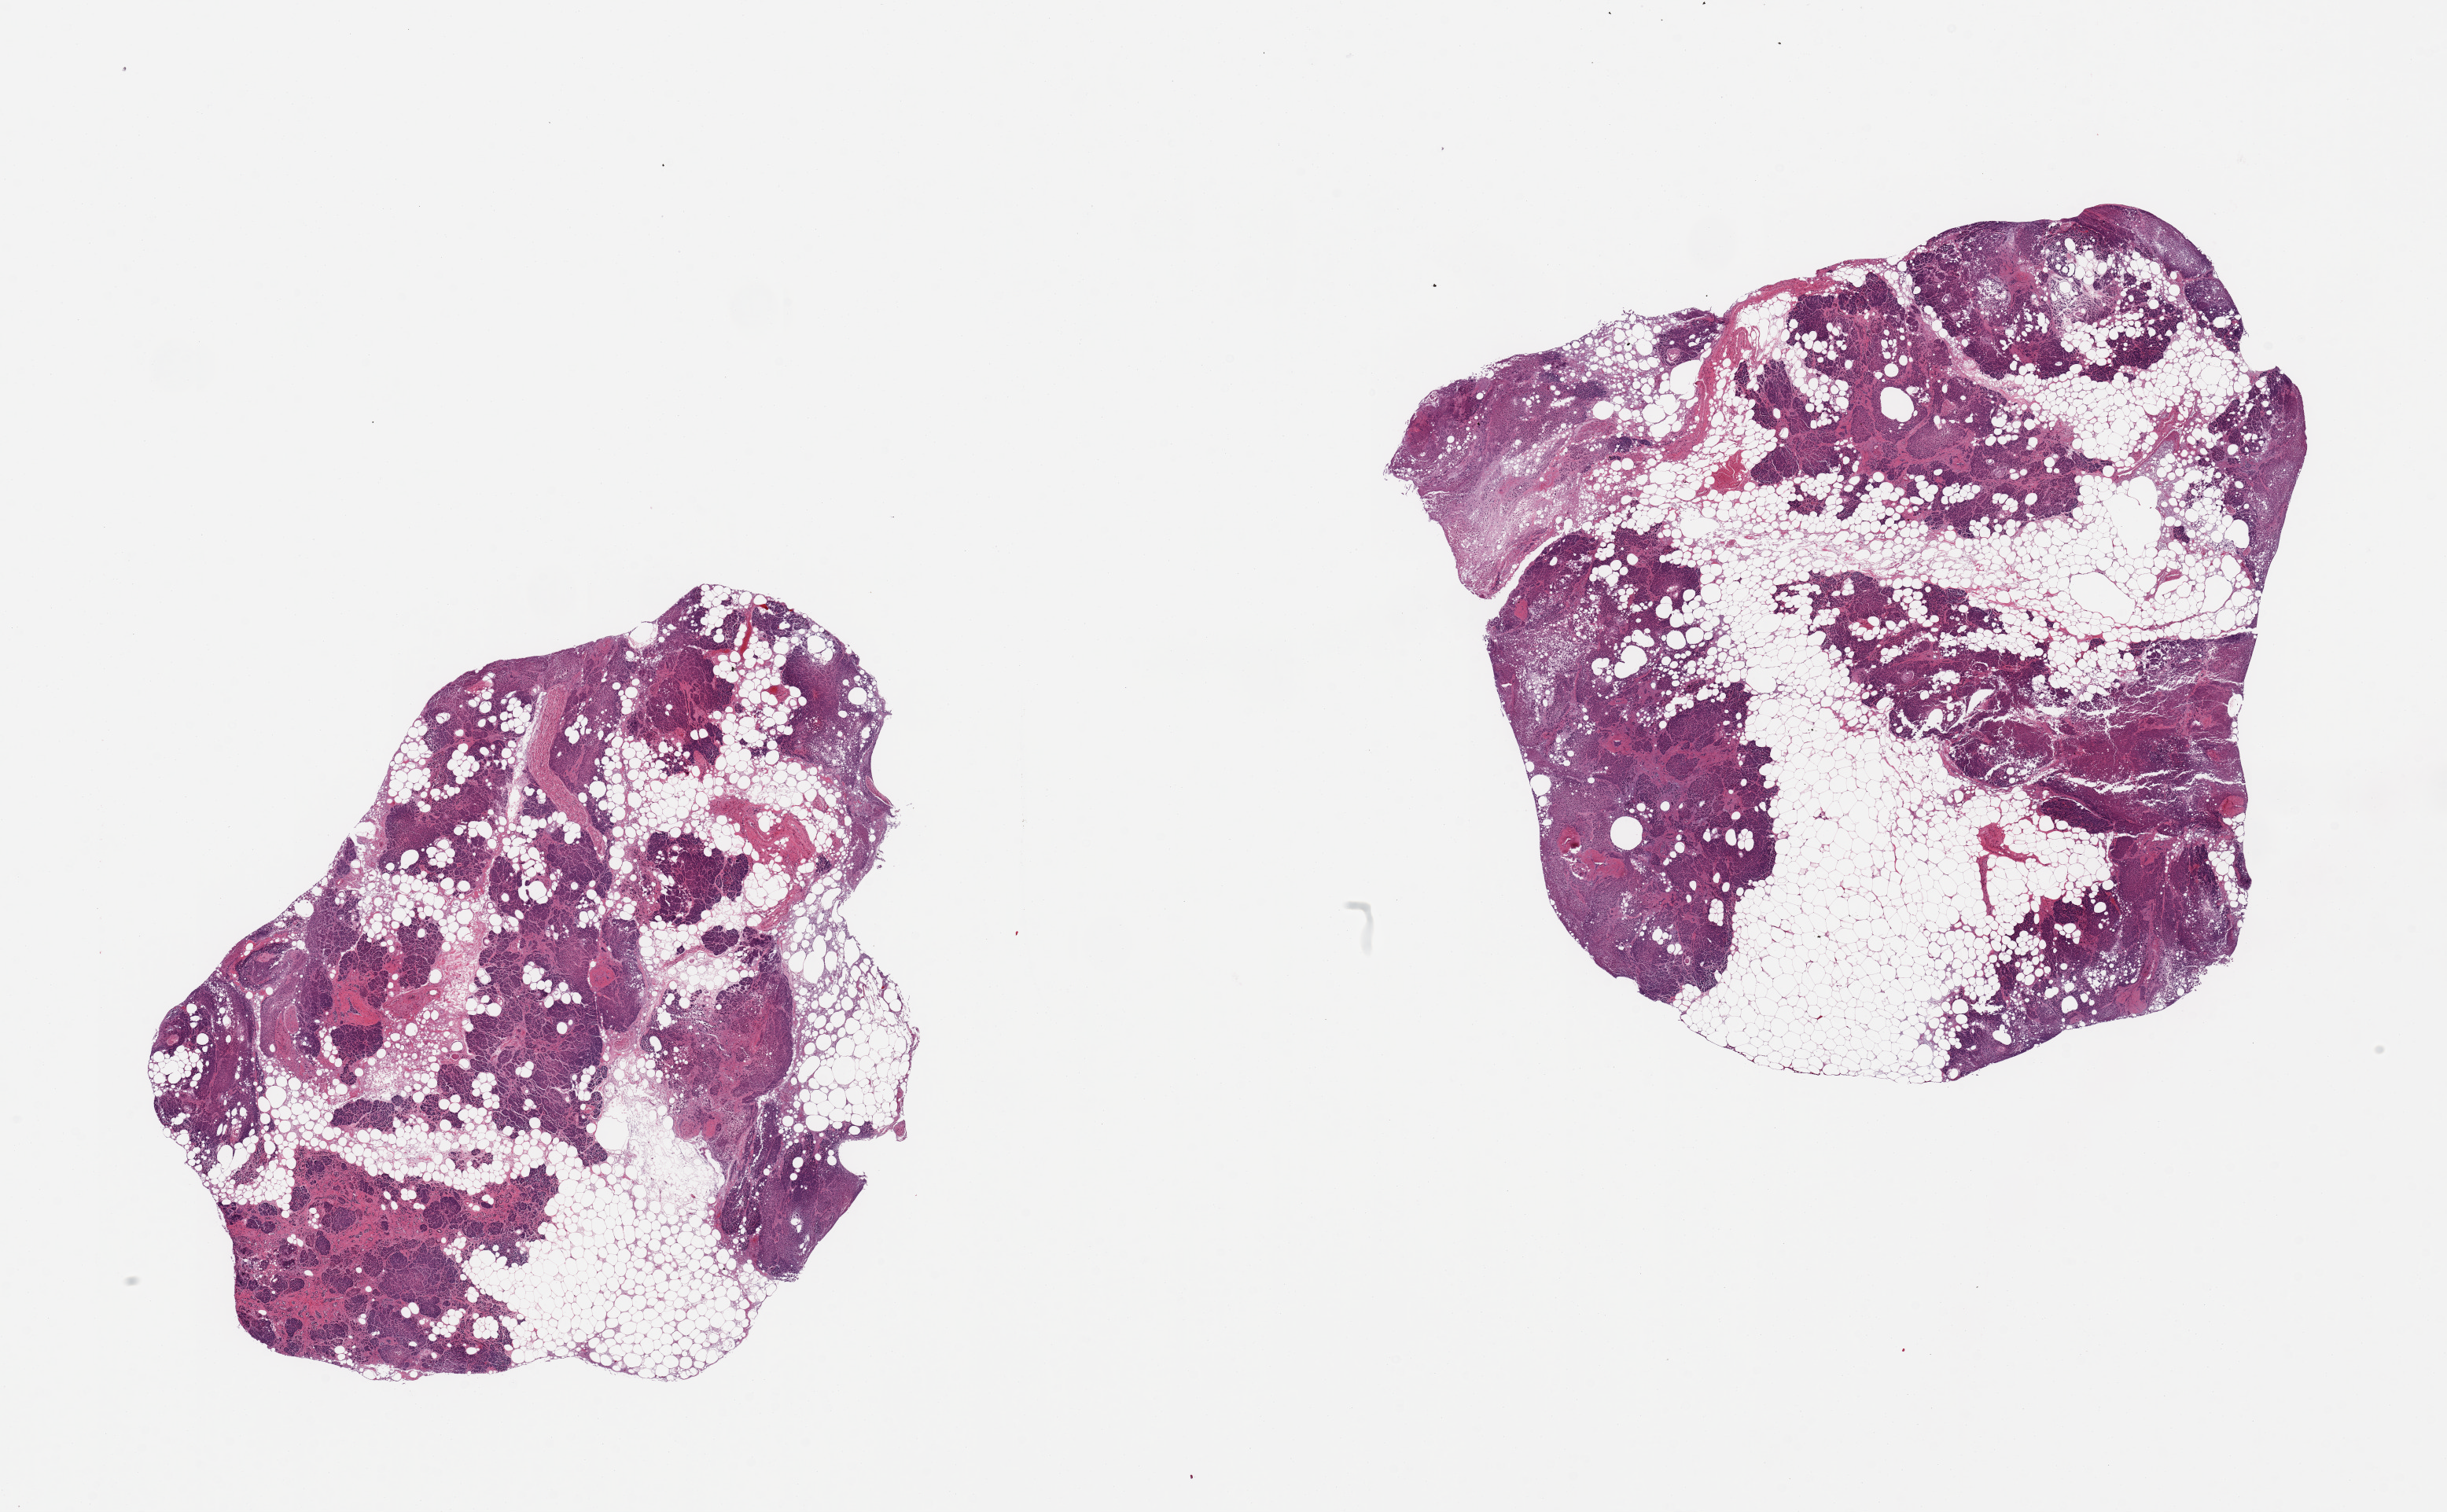
Digitized H&E-stained section, brightfield — a low-resolution overview of the entire scanned area, about 24.6 x 15.2 mm (acquisition: 20x scan). PAXgene-fixed paraffin-embedded (PFPE) section. Section of pancreas (target tissue). Donor tissue sample.
- pathologist's review note for this sample: 2 pieces; ~50% internal and attached fat, some atrophy/fibrosis, saponification